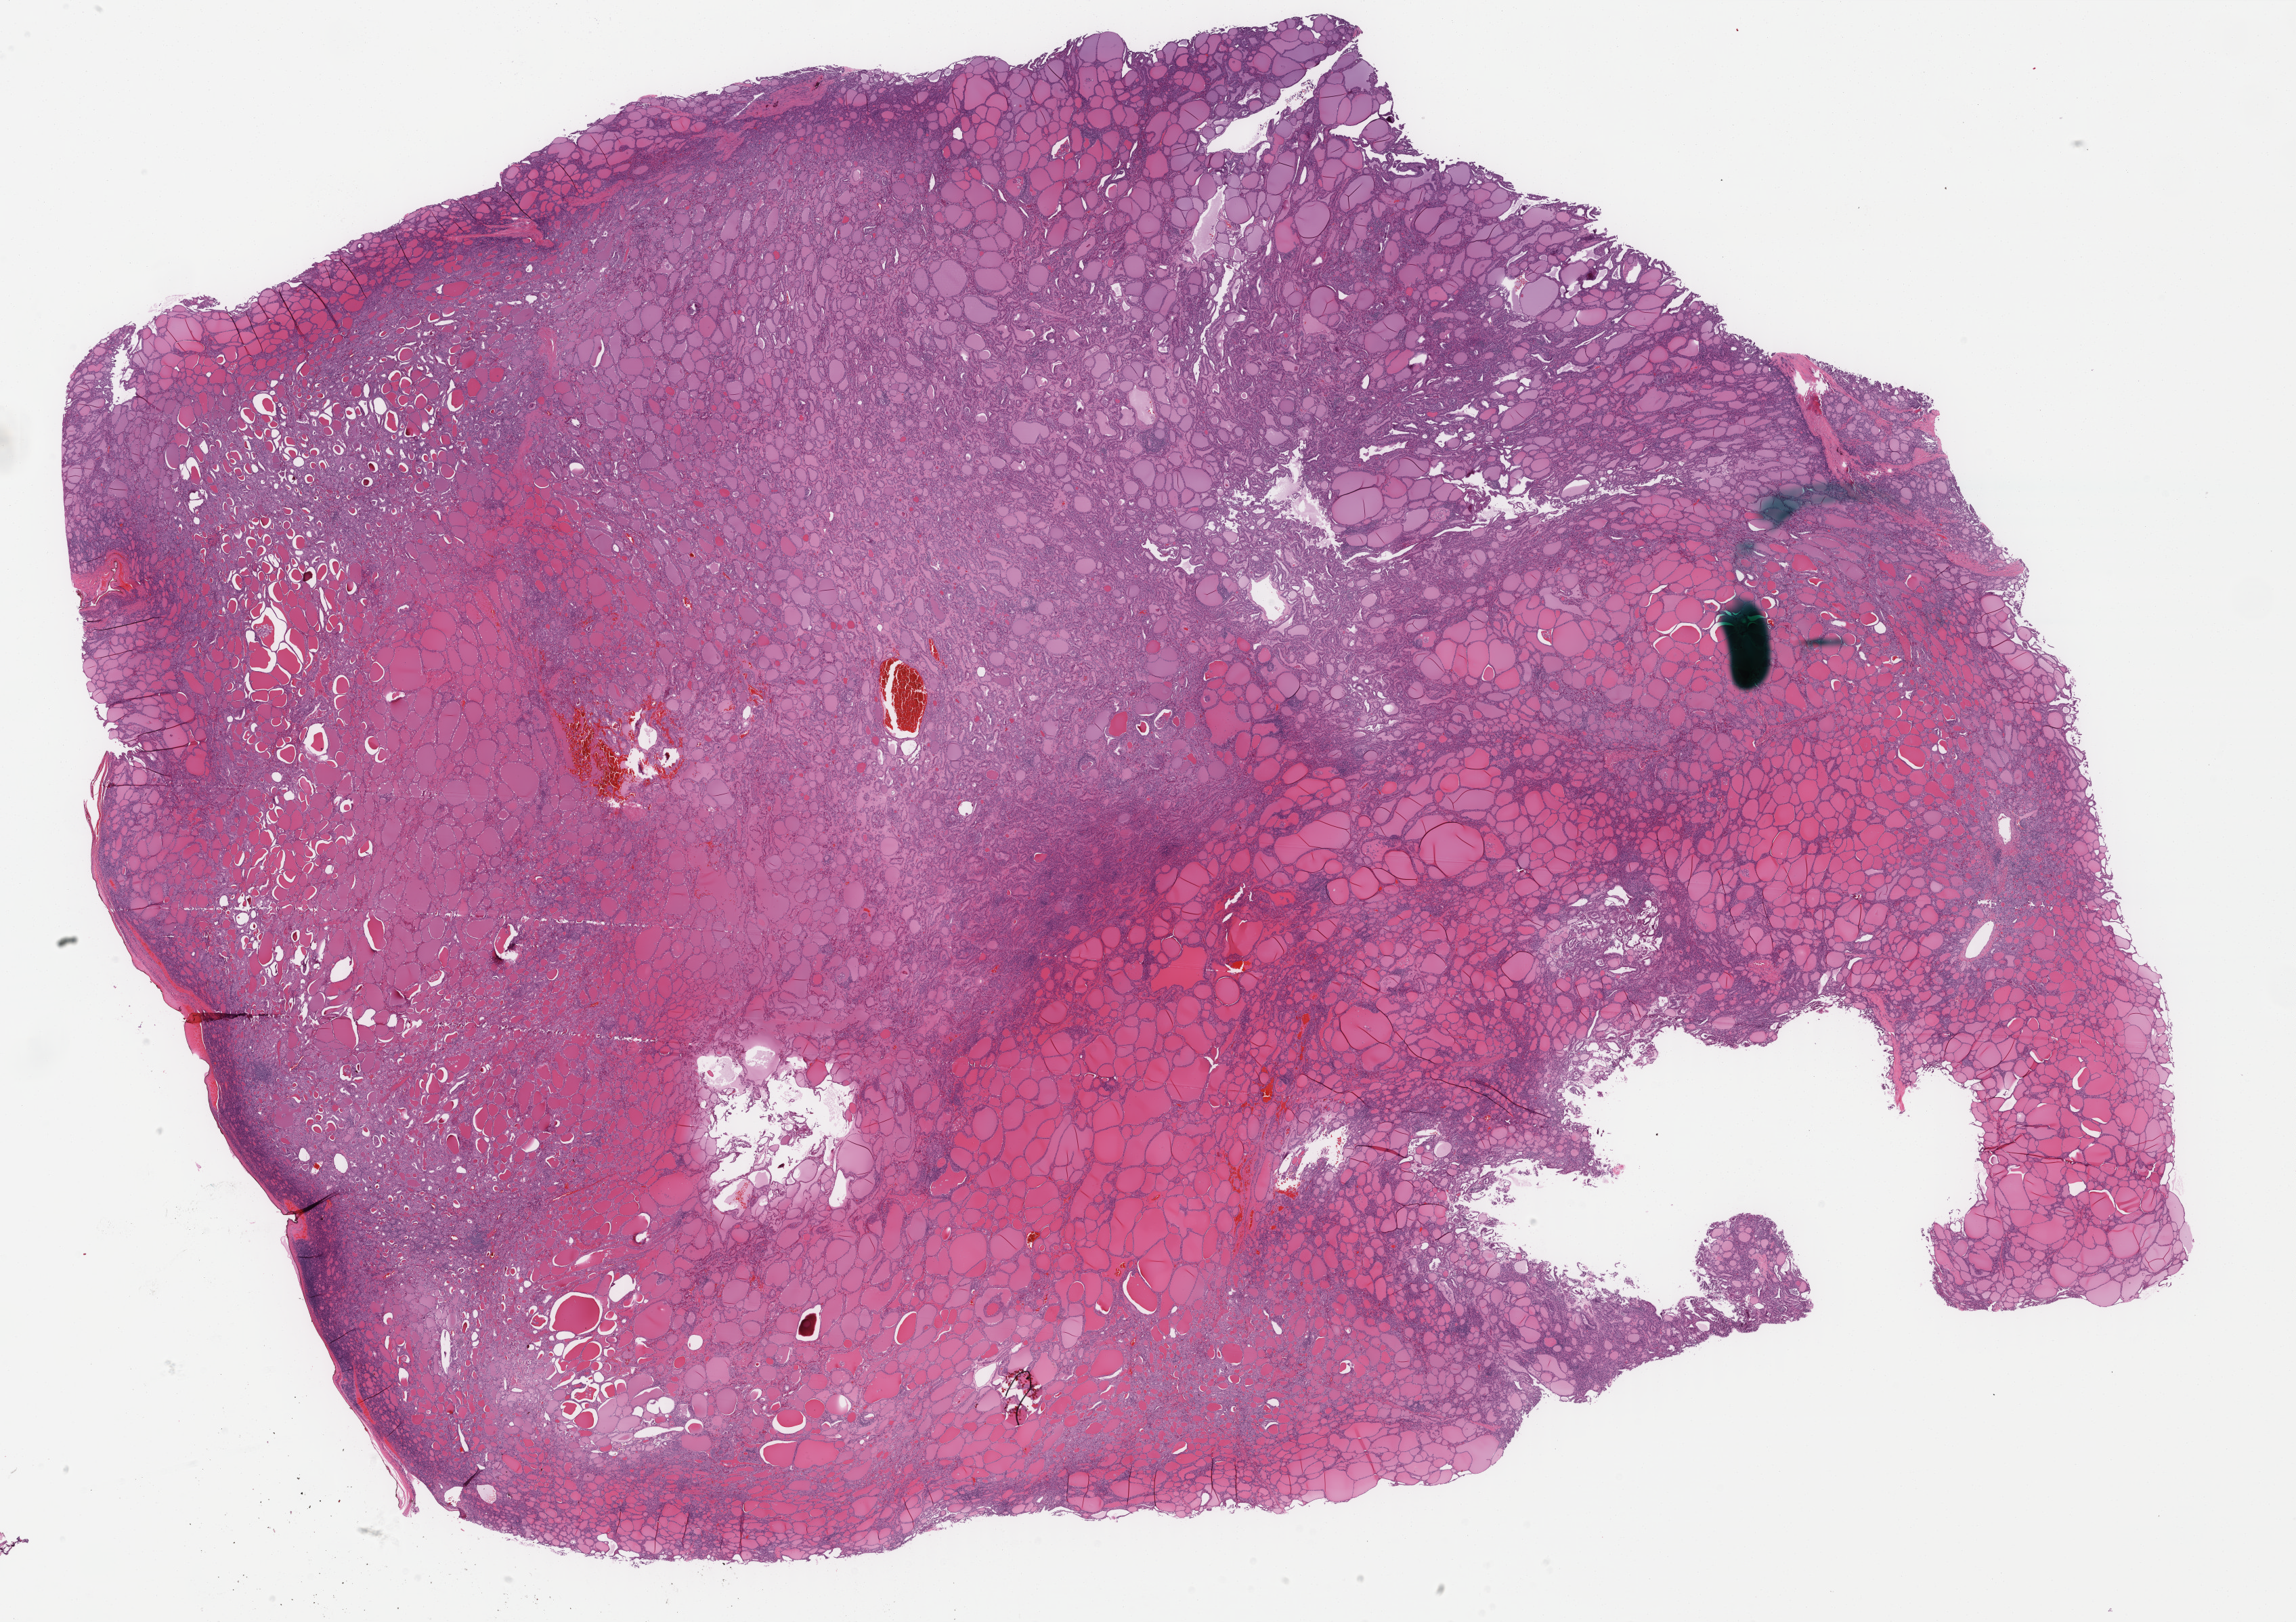
Whole-slide histology image, Hematoxylin and eosin (H&E) stained, low-resolution overview of the scanned area, about 26.9 x 19.0 mm (acquisition: 40x scan). Formalin-fixed paraffin-embedded (FFPE) diagnostic section. Primary tumour sample from the thyroid. Male patient; age at initial diagnosis 50 years.
Lymph nodes positive (case pathology): 0 of 2 examined. TNM: T3 N0 M0. Histologic diagnosis: Papillary carcinoma, follicular variant (thyroid gland). AJCC pathologic stage: III (7th edition).